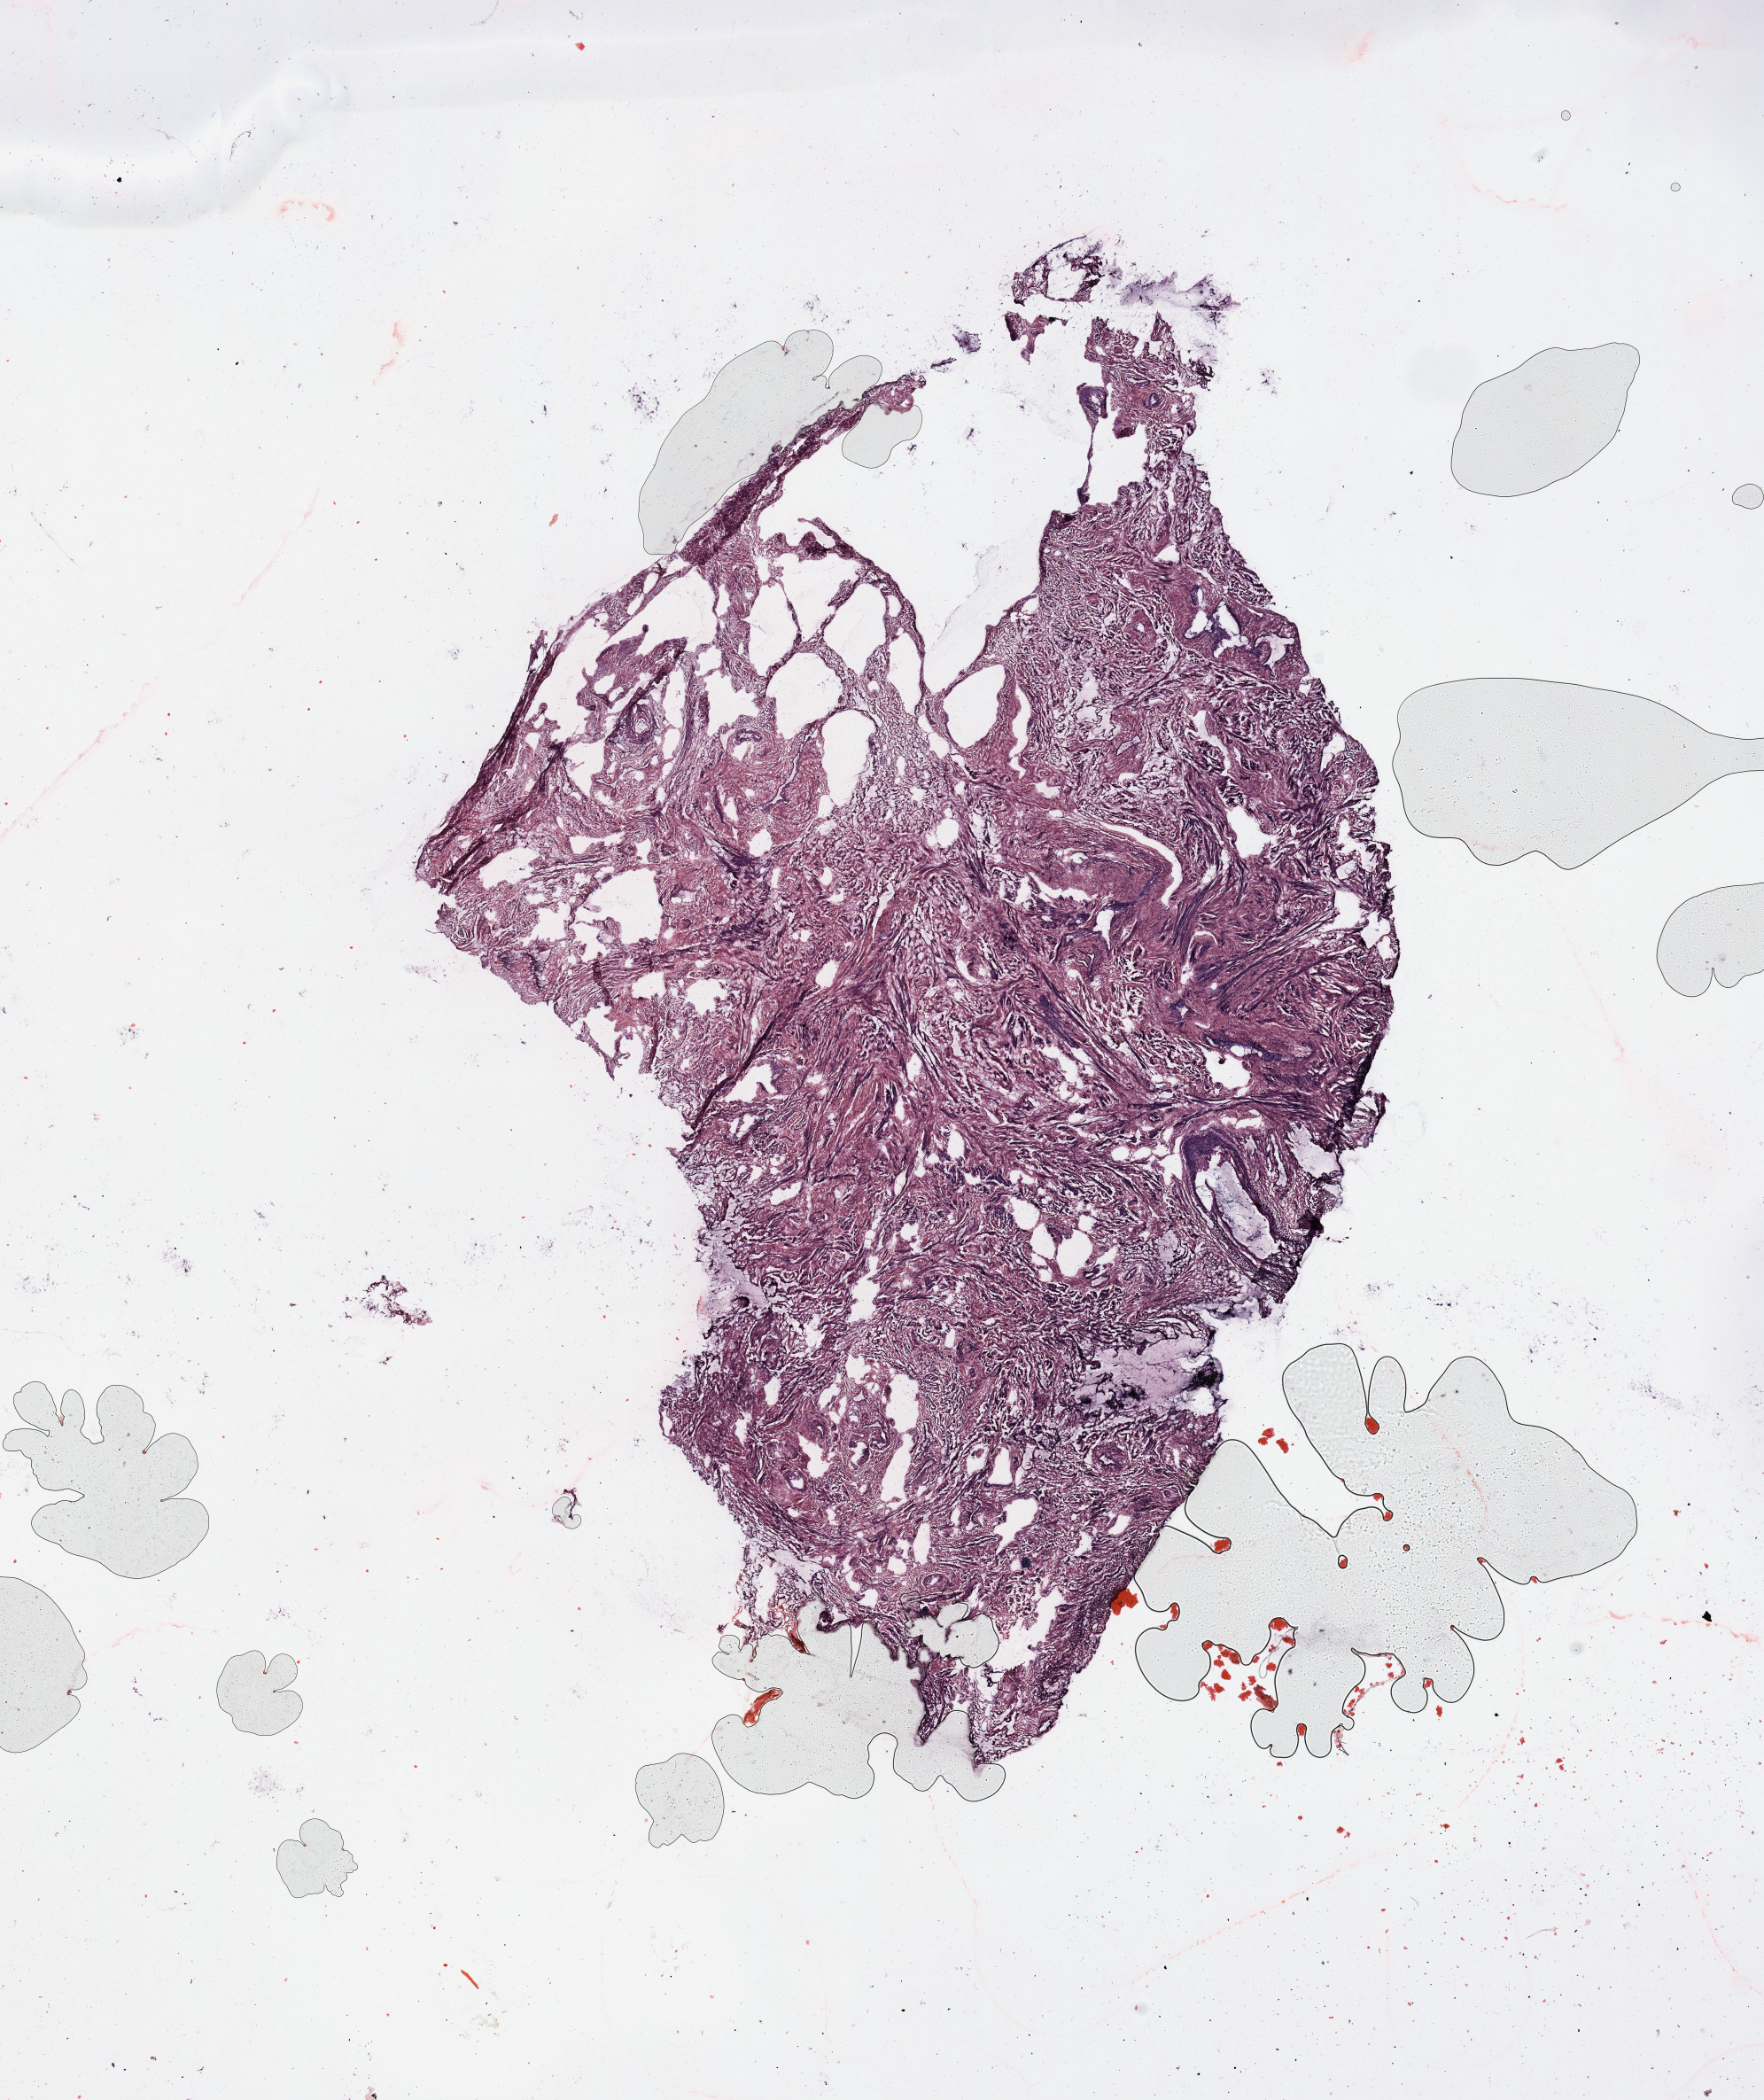
Digitized H&E tissue section (whole slide), whole scanned area (about 15.8 x 18.7 mm, acquisition: 20x scan) shown as a low-resolution overview; uterus, tissue type not recorded. Patient: female, age 62 years.
Patient diagnosis: Endometrioid adenocarcinoma, NOS.